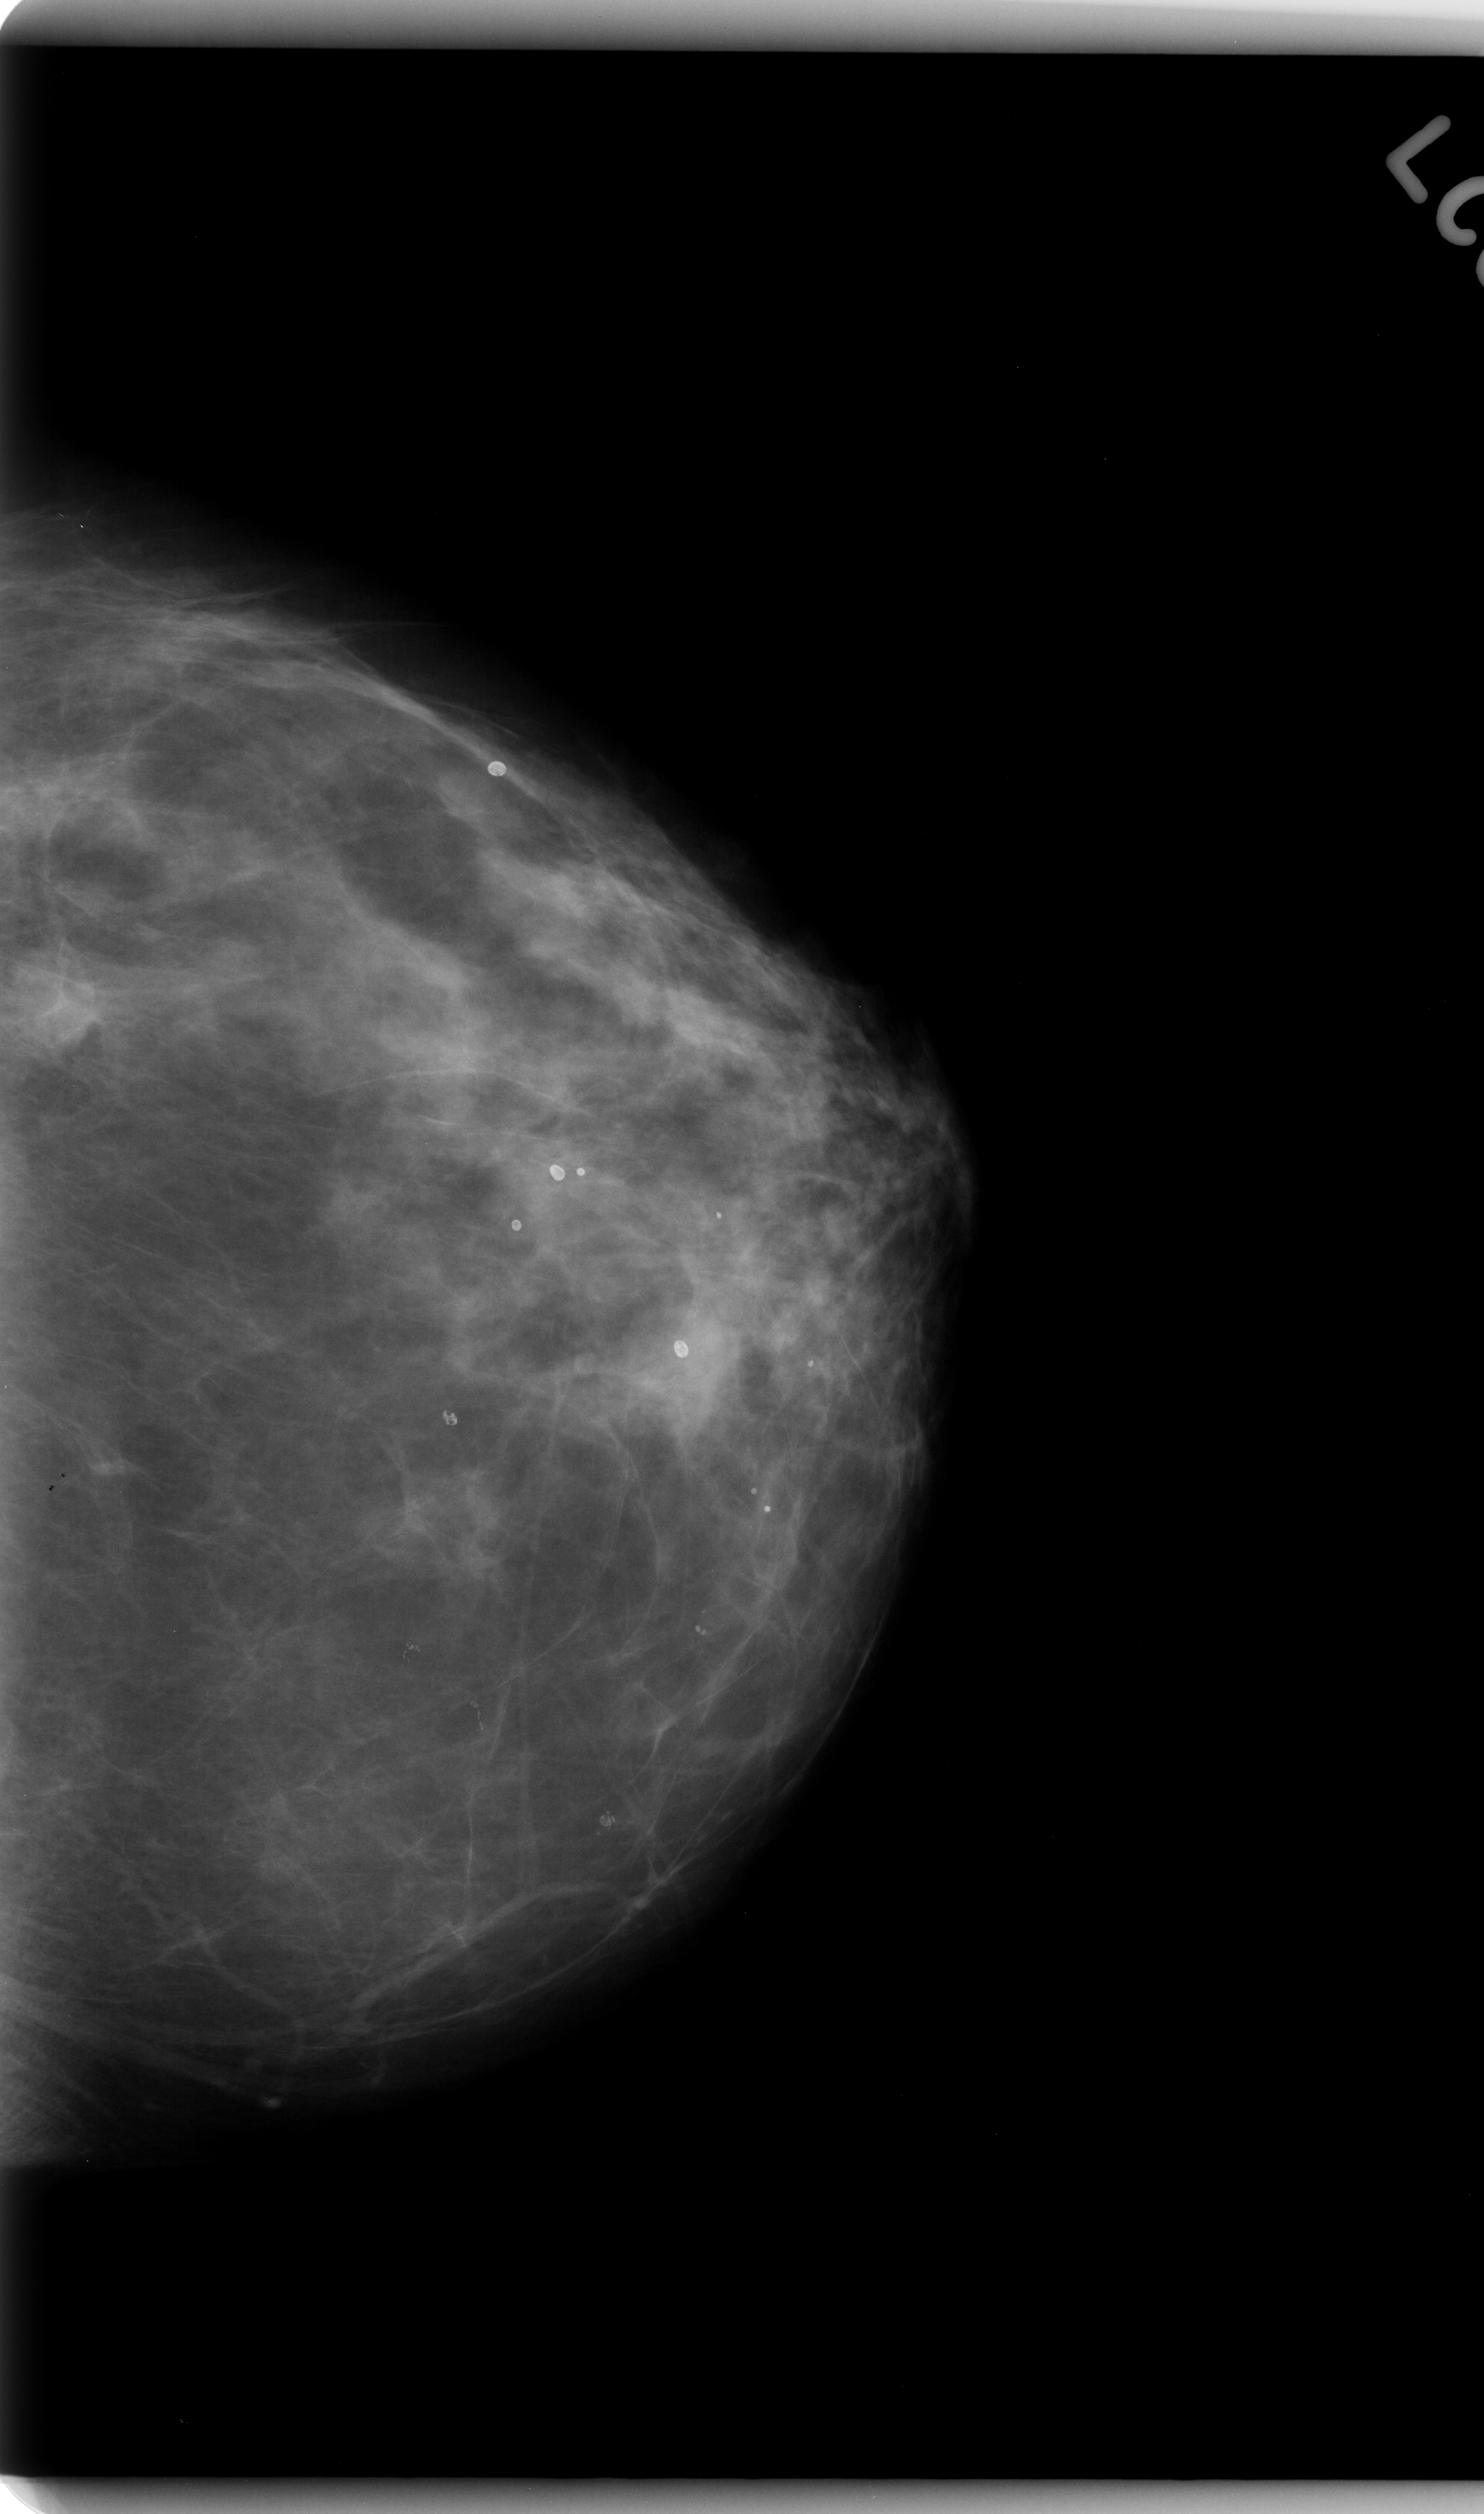
Digitized screen-film mammogram, left breast, CC view, BI-RADS breast density category 2 (scale 1–4).
Finding: mass, shape lobulated, margins ill defined; BI-RADS assessment category 5; subtlety rating 4 on a 1 (subtle) to 5 (obvious) scale; pathology result (as recorded, not read from the image): malignant.